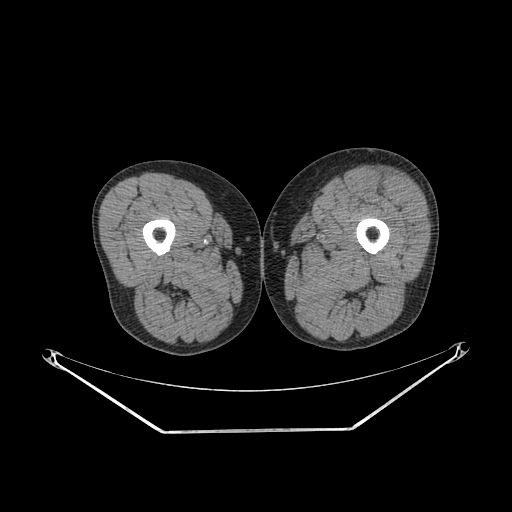
CT of an extremity soft-tissue mass (from a PET/CT study), one axial slice. Position 216 of 267 along the scan axis. Reconstruction kernel SOFT. 140 kVp. Soft-tissue window (W 400 / L 40 HU). 3.75 mm slice thickness. 512 × 512 image matrix, field of view 500 × 500 mm. Male patient. From the clinical record (not read from this slice): histological type: extraskeletal osteosarcoma; grade: high; site of the primary tumour: thigh.
Annotated regions visible in this slice (expert contour drawn on MRI and transferred to this co-registered scan by the dataset authors):
- gross tumour volume (mass): bounding box [x1, y1, x2, y2] px = [390, 180, 396, 195]